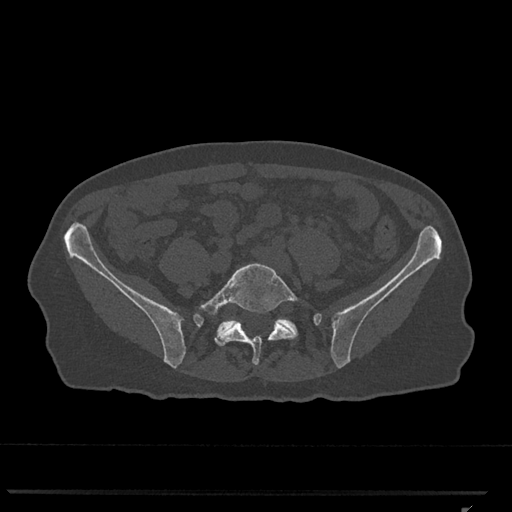
CT including the spine, one axial slice; slice 141 of 793 in the series (ordered by position); reconstruction kernel Br40s/3; bone window (W 1800 / L 400 HU); 512 × 512 image matrix, field of view 380 × 380 mm. Patient: female, 62 years. From the clinical record (not read from this slice): primary cancer: renal.
Annotated regions visible in this slice (semi-automatic segmentation, software-assisted and operator-edited):
- L5 vertebra: bounding box (x1, y1, x2, y2) in pixels: (199, 263, 306, 365)